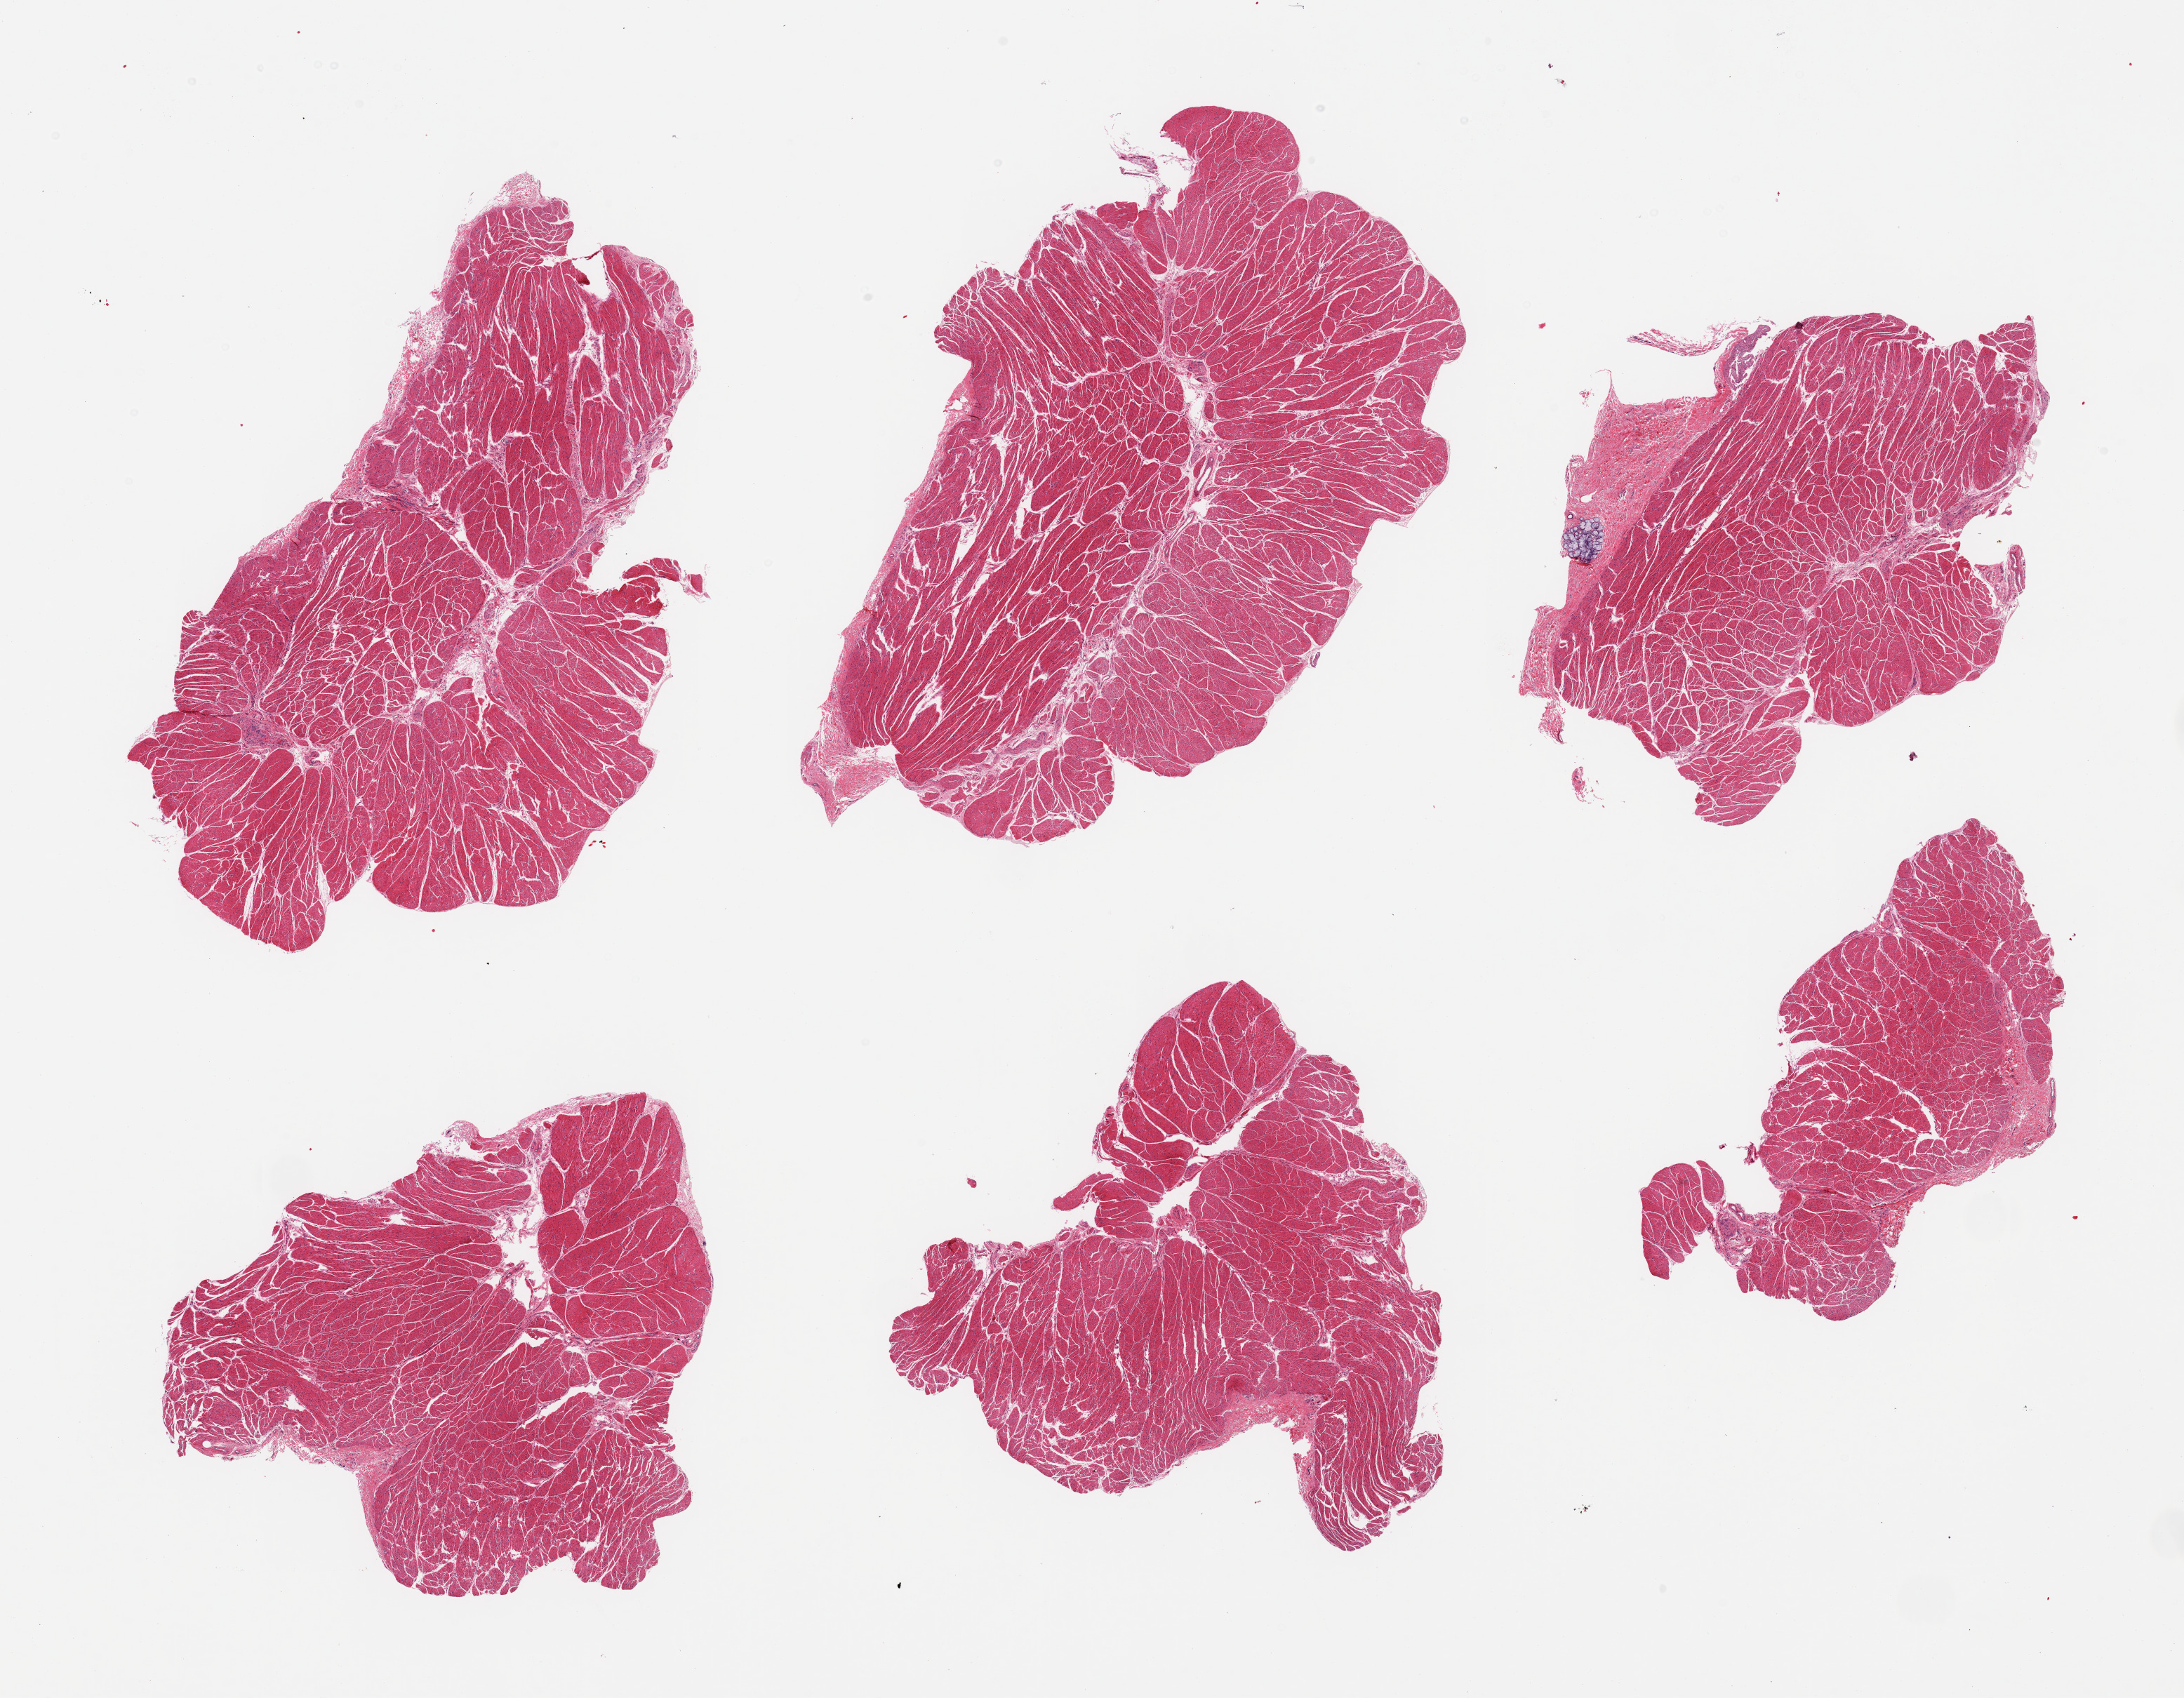
Digitized hematoxylin and eosin (H&E)-stained section, shown as a low-resolution overview of the whole scanned area (about 24.6 x 19.1 mm); PAXgene-fixed paraffin-embedded (PFPE) section; target tissue: esophageal mucous membrane; tissue donor sample. Male donor.
Review note (as recorded): 6 pieces; muscularis, not mucosa; single focus of submucosal glands and detached fragment of squamous epithelium.